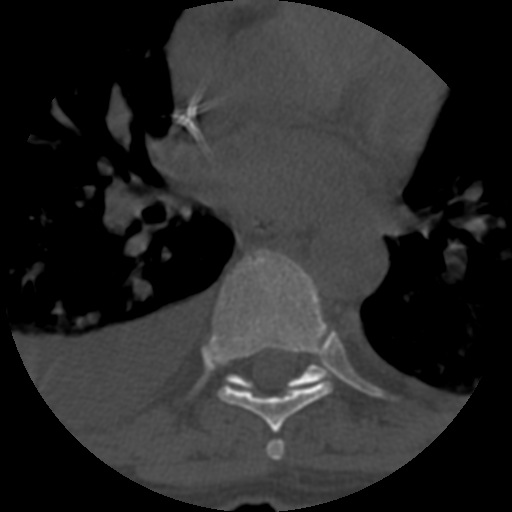
CT including the spine, one axial slice; position 411 of 708 along the scan axis; reconstruction kernel STANDARD; 120 kVp; one of 3 acquisitions stored at this slice position; bone window (W 1800 / L 400 HU); 1.25 mm slice thickness; 512 × 512 image matrix. Patient age 55 years. Case-level facts recorded for this patient, not image findings: primary cancer: colon.
Structures marked on this image (semi-automatically segmented with operator editing):
- T6 vertebra: bounding box (x1, y1, x2, y2) in pixels: (266, 440, 285, 461)
- T7 vertebra: (212, 250, 333, 433)
- T8 vertebra: (226, 365, 330, 392)